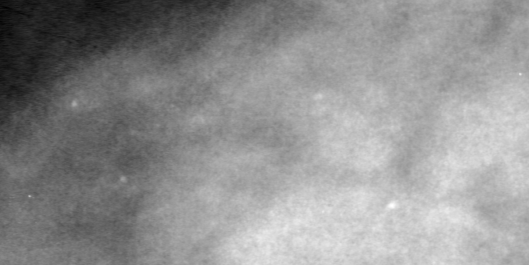
Region of interest cut from a scanned film mammogram (one marked finding); left breast; CC view.
Finding: calcifications, morphology punctate, distribution linear; BI-RADS assessment category 4; subtlety rating 1 on a 1 (subtle) to 5 (obvious) scale; pathology (as recorded): benign.